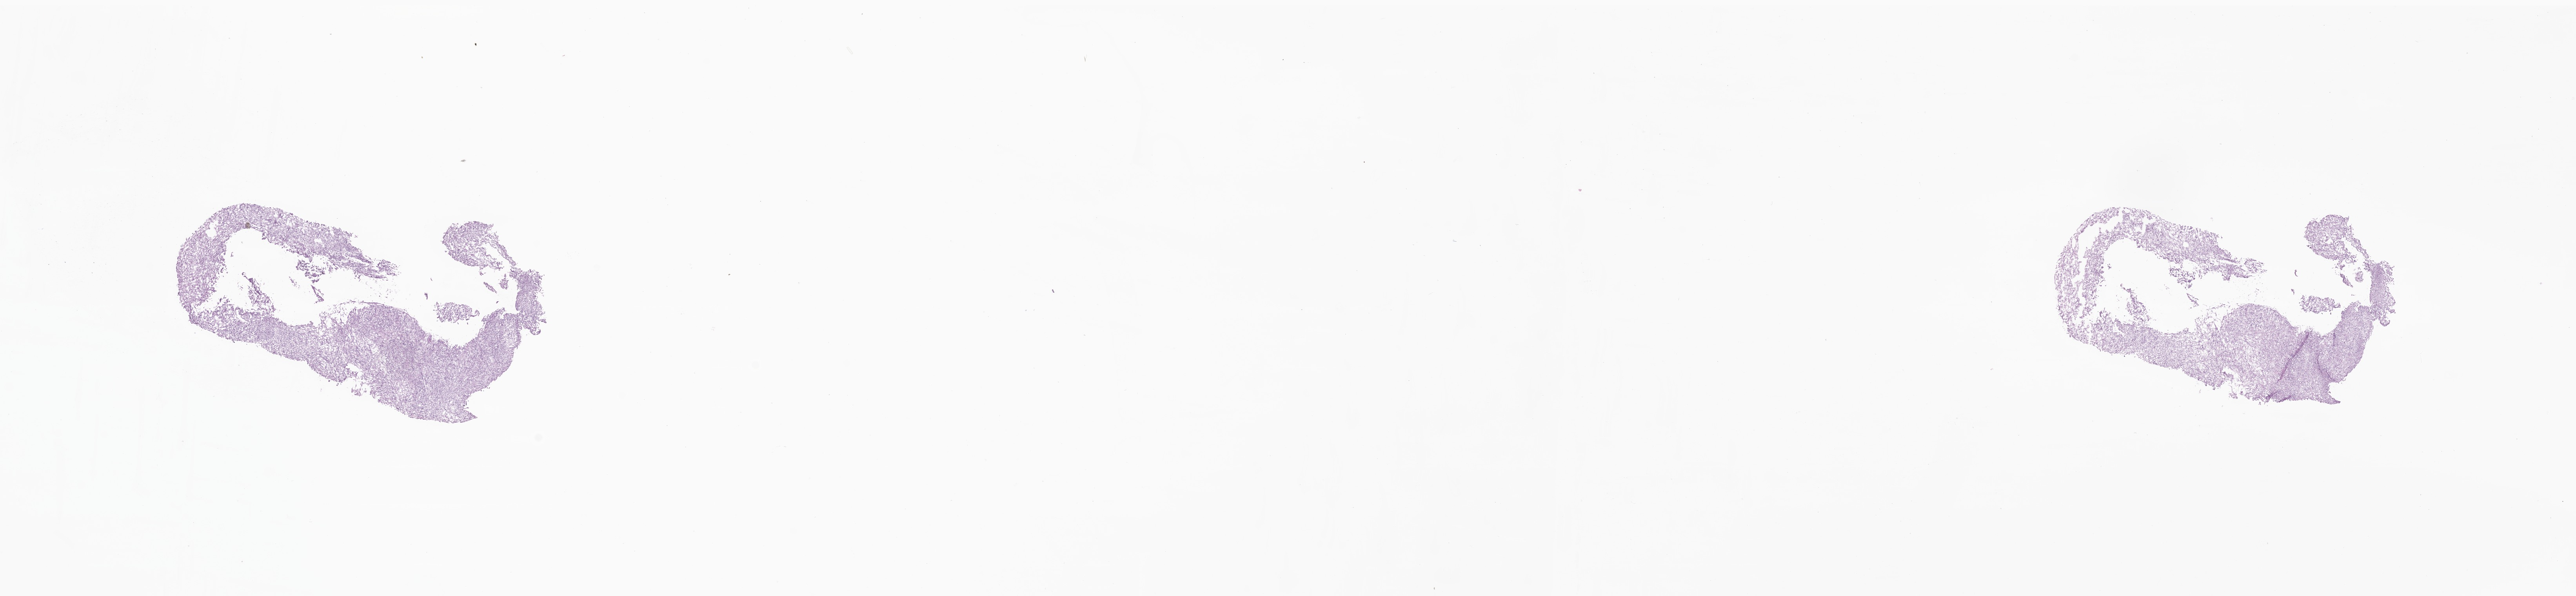
Haematoxylin and eosin whole-slide image of tumor tissue from the brain — low-resolution overview of the scanned area, about 27.5 x 6.4 mm. Frozen section. Patient: female, age 176 months.
Diagnosis (ICD-O-3 morphology term): Meningioma, malignant.